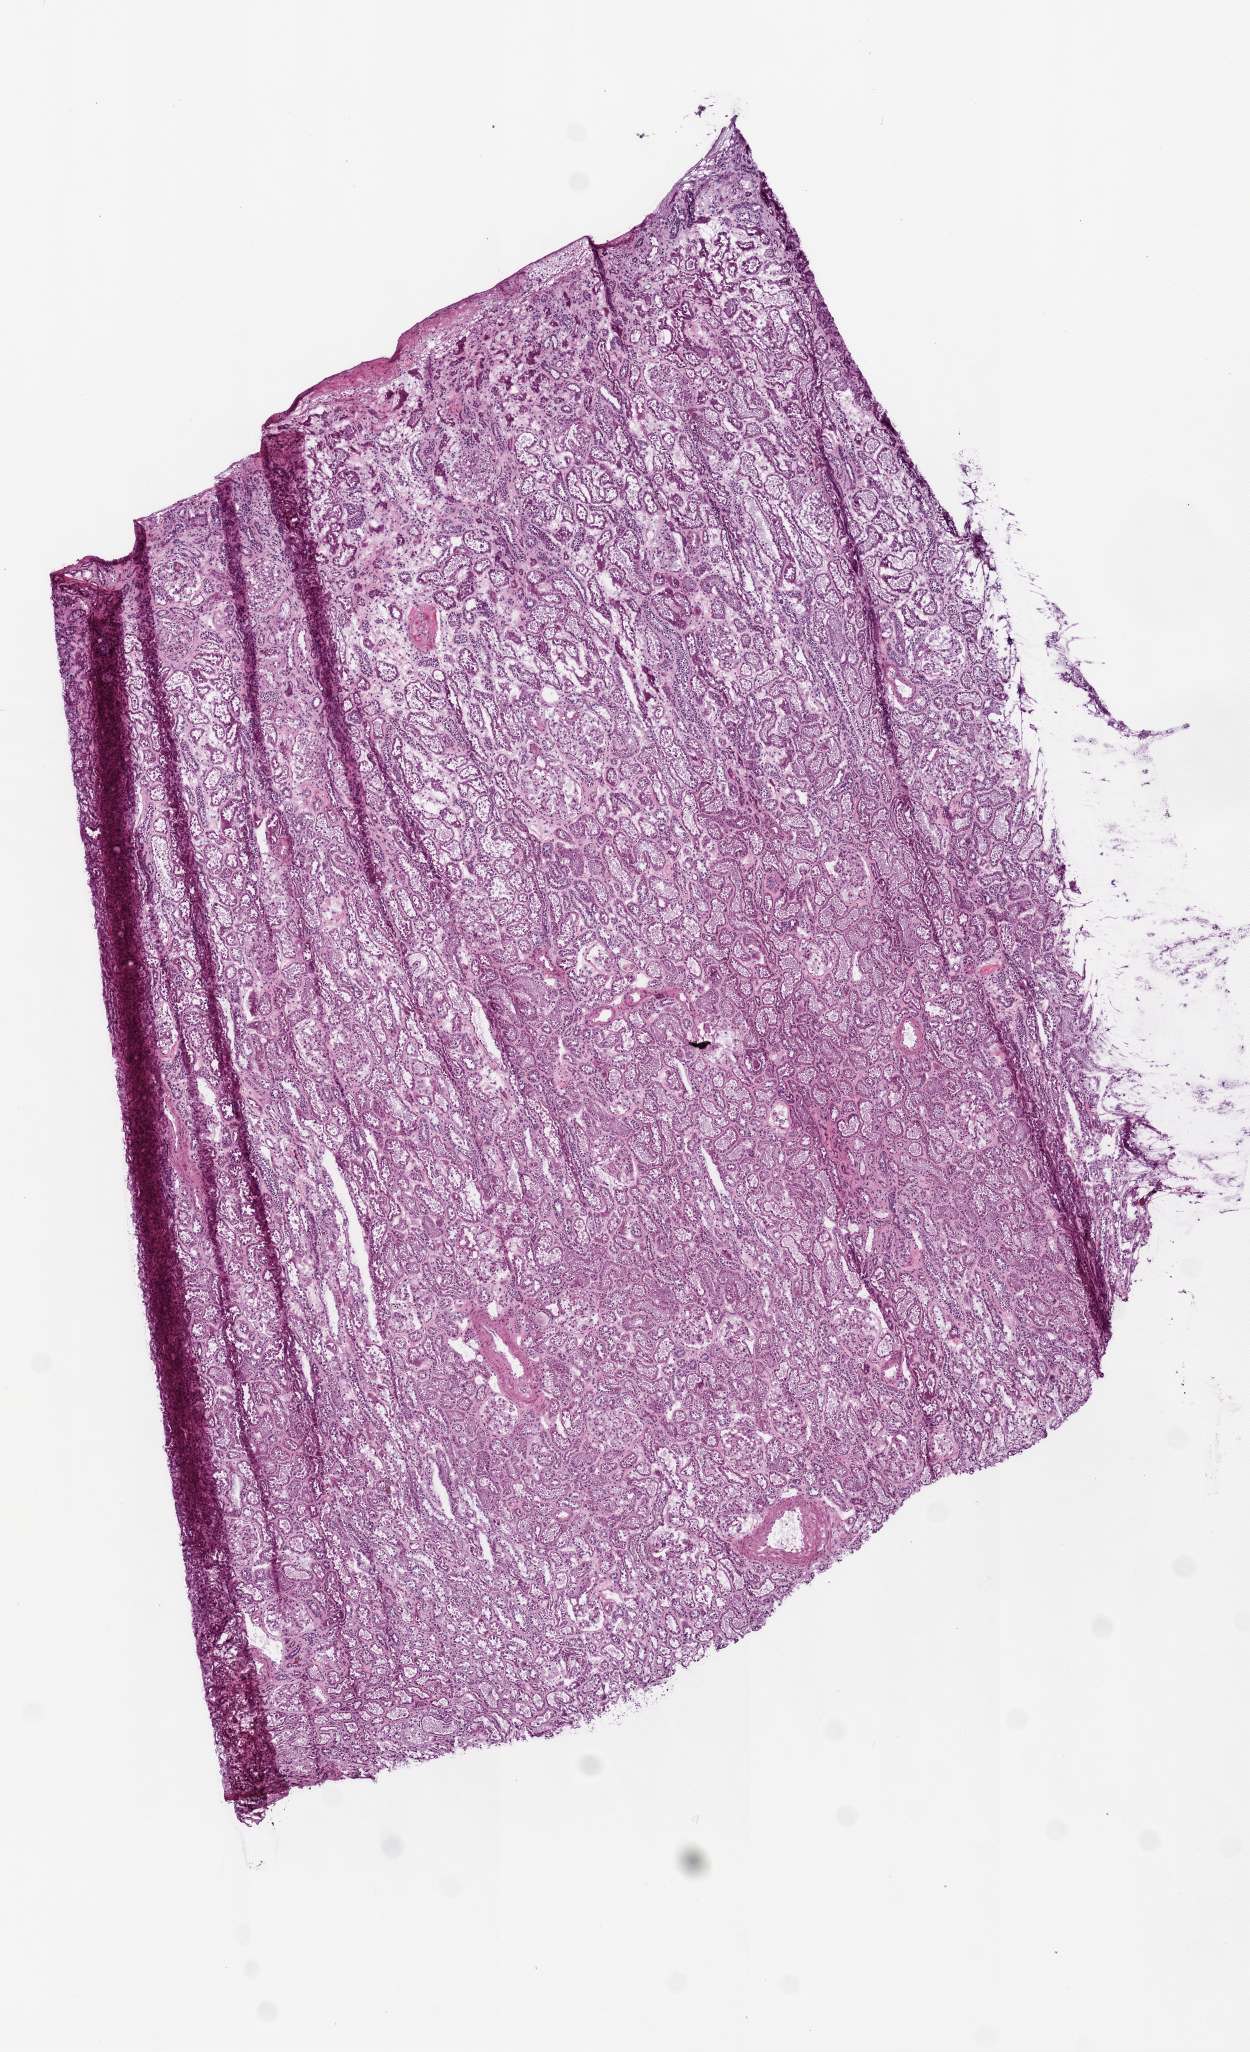
Digitized Hematoxylin and eosin (H&E) stained tissue section (whole slide), whole scanned area (about 5.0 x 8.2 mm, acquisition: 20x scan) shown as a low-resolution overview. Frozen section from the top of the tissue portion. Sample: solid tissue normal (non-tumour tissue), kidney. Patient: female, age at initial diagnosis 78 years.
This section: solid tissue normal sample (biorepository sample class). Patient diagnosis: Clear cell adenocarcinoma, NOS.